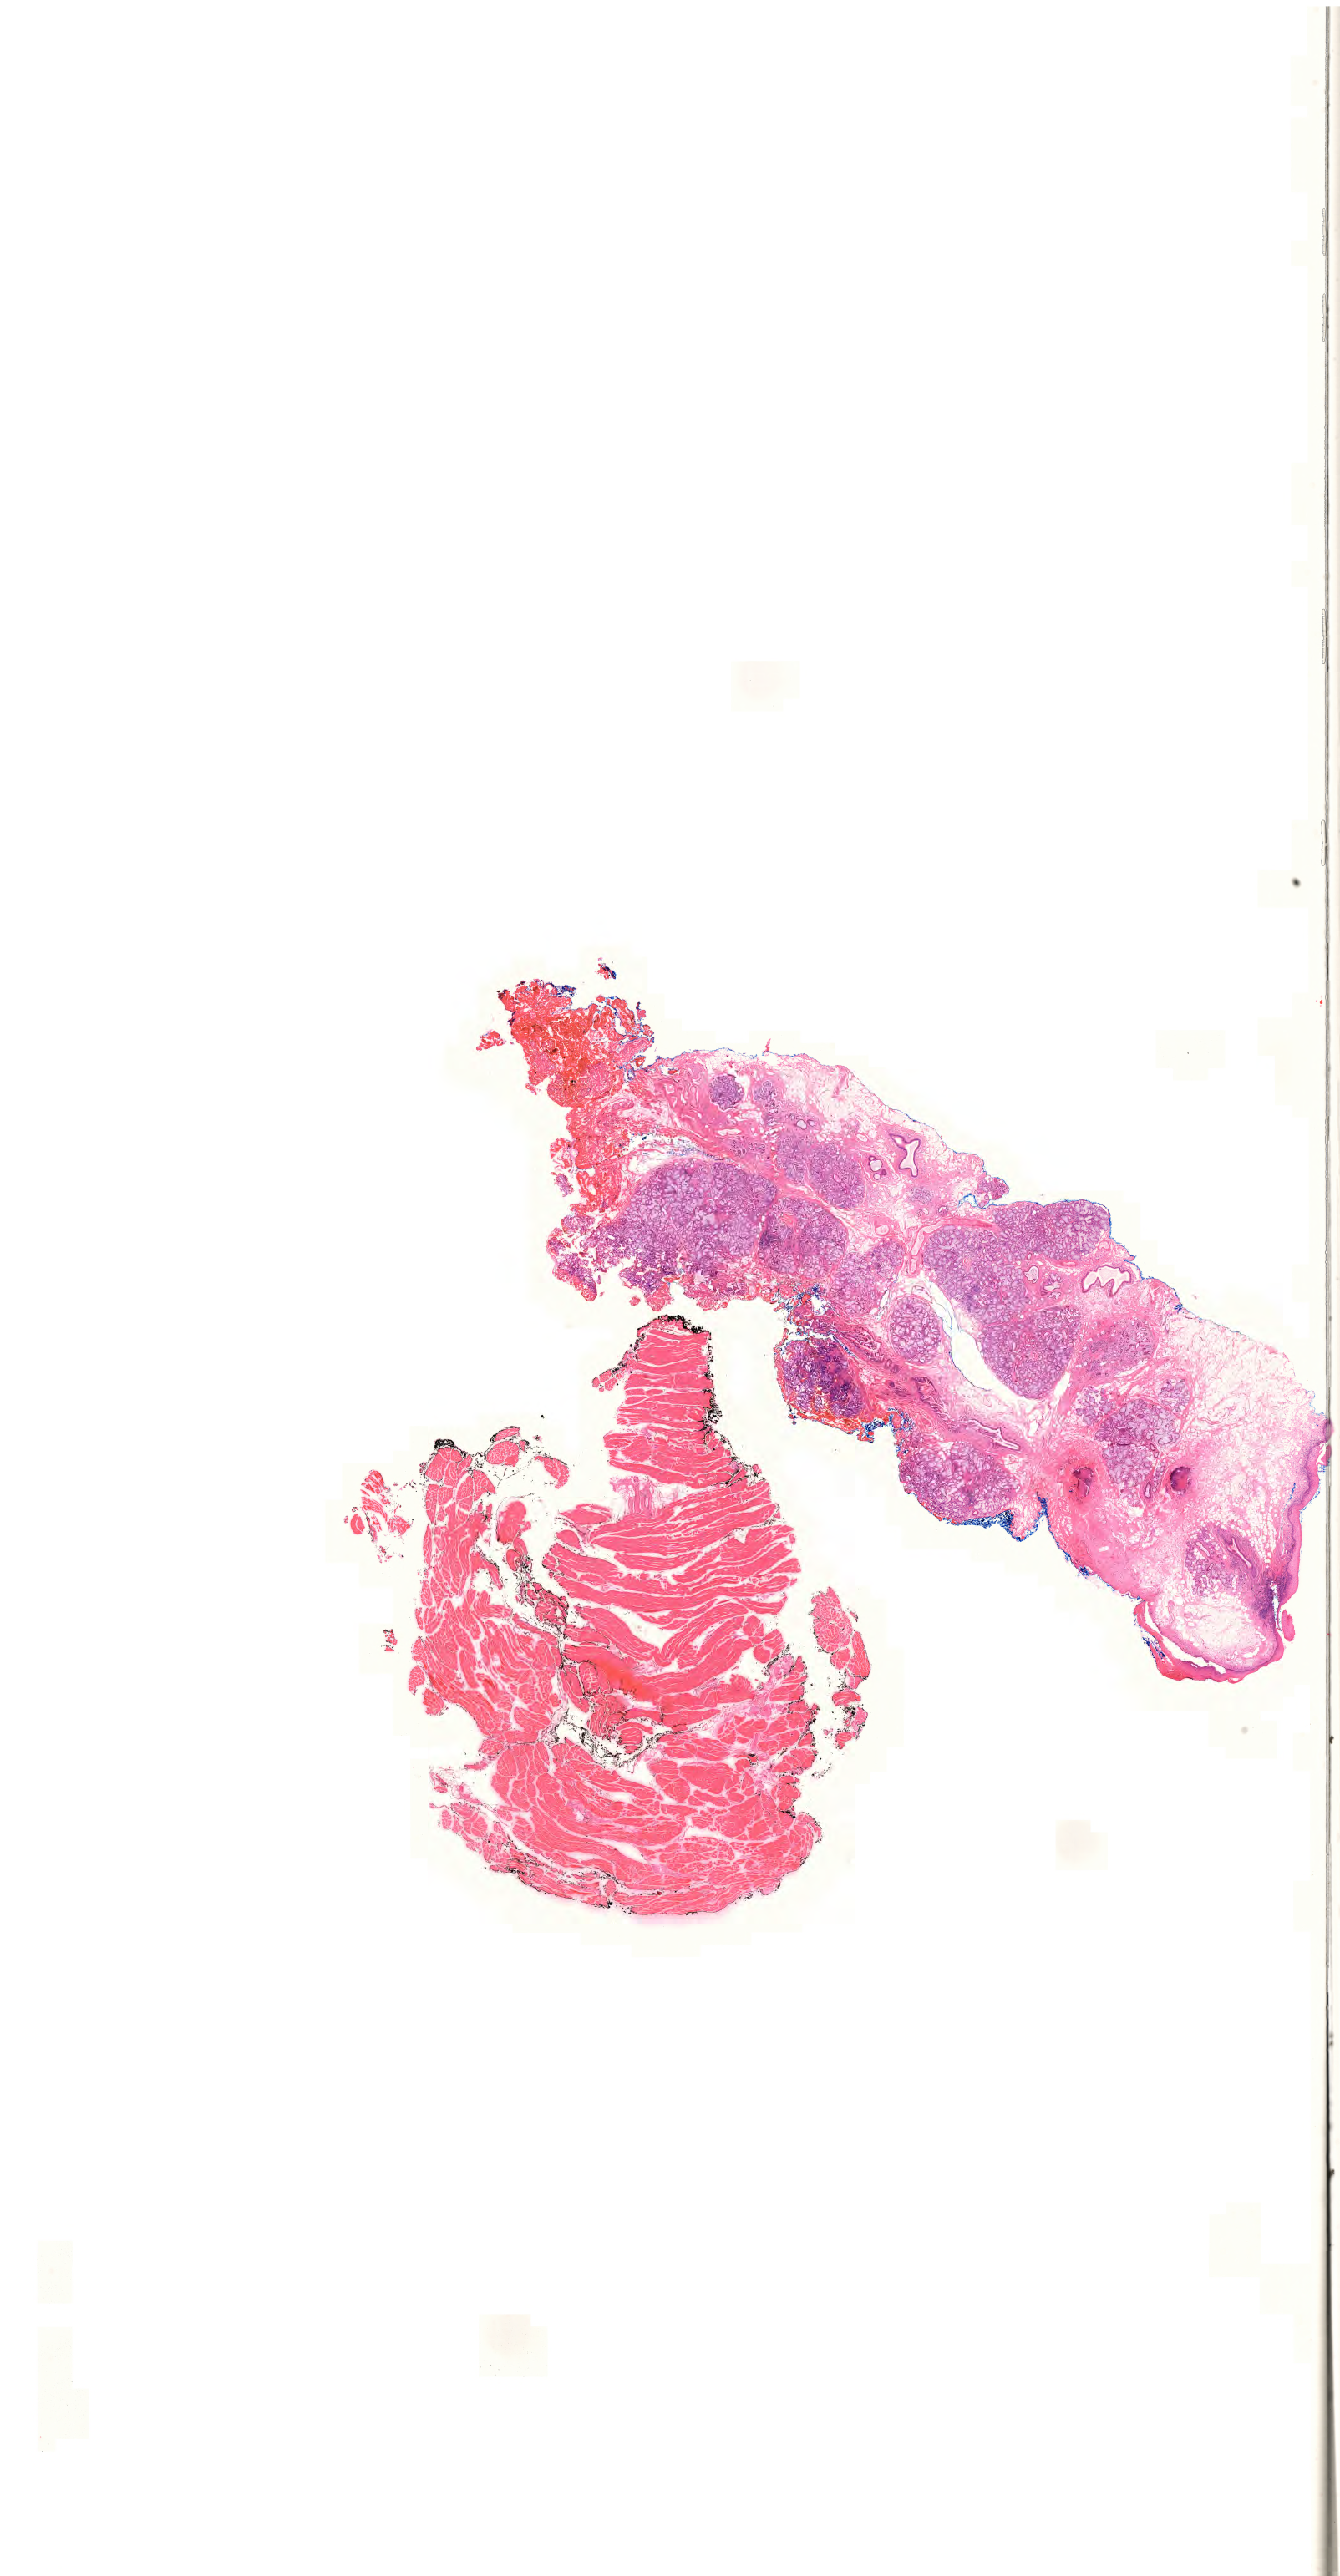
Whole-slide histology image, Hematoxylin and eosin (H&E) stained, a low-resolution overview of the entire scanned area, about 23.9 x 45.9 mm (slide scanned at 20x), formalin-fixed paraffin-embedded (FFPE) diagnostic section, primary tumour sample from the head and neck. Male, age 79 years at initial diagnosis. Histologic grade: G3 (poorly differentiated).
Laterality: midline. AJCC pathologic stage: IVA (7th edition). Diagnosis: Squamous cell carcinoma, NOS (floor of mouth, NOS).